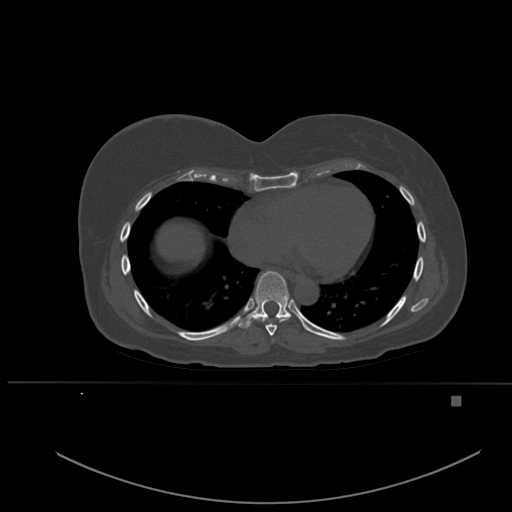
CT including the spine, one axial slice; slice 326 of 651 in the series (ordered by position); bone window (W 1800 / L 400 HU); 1.5 mm slice thickness; 512 × 512 image matrix, field of view 443 × 443 mm. Patient: female, 49 years. From the clinical record (not read from this slice): primary cancer: breast.
Outlined on this slice (semi-automatically segmented with operator editing):
- T7 vertebra: box from (x=262, y=320) to (x=284, y=336) px
- T8 vertebra: (x=237, y=271)–(x=291, y=329)